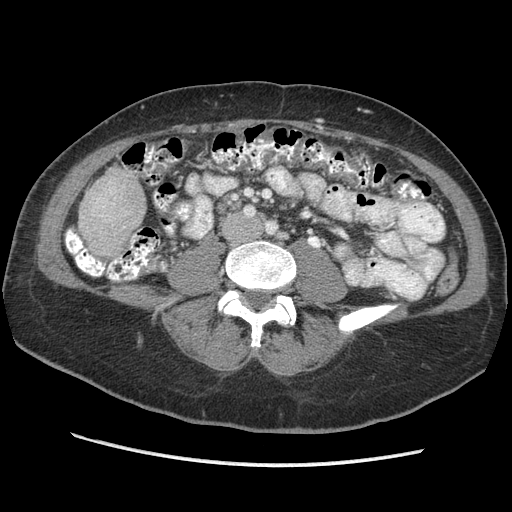
Contrast-enhanced abdominal CT (liver protocol), one axial slice. Position 84 of 170 along the scan axis. Reconstruction kernel STANDARD. Soft-tissue window (W 400 / L 40 HU). 512 × 512 image matrix, field of view 360 × 360 mm. Case-level facts recorded for this patient, not image findings: diagnosis: hepatocellular carcinoma (patient treated with transarterial chemoembolisation; whether this scan precedes or follows treatment is not stated here); TNM stage (as recorded): Stage-II; Child-Pugh class: A; tumour nodularity: multinodular.
Outlined on this slice (semi-automatically segmented with operator editing):
- liver parenchyma outside the tumour (the mass and vessels are separate outlines, so this box may not span the whole liver): bounding box (x1, y1, x2, y2) in pixels: (78, 168, 146, 256)
- liver vessels: (96, 189, 112, 207)